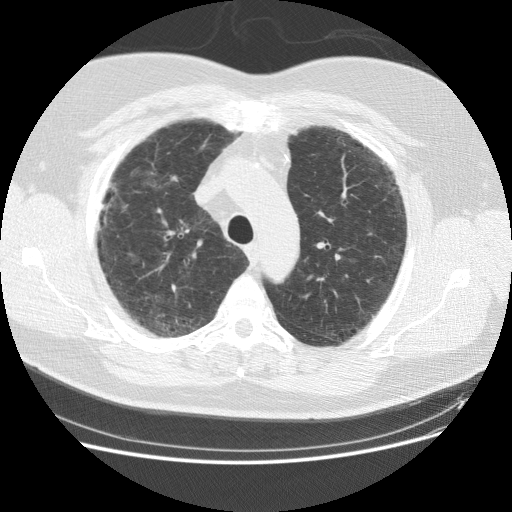
Chest CT (low-dose screening protocol), one axial image, baseline screening round, lung window (W 1500 / L -600 HU), 2.5 mm slice thickness, standard (soft-tissue) reconstruction kernel (STANDARD), 120 kVp, slice 33 of 151 in the series, 512 × 512 image matrix. Male, age 59 years at enrolment. Current smoker at enrolment.
Expert-annotated lung lesion, bounding box [x1, y1, x2, y2] px = [87, 165, 141, 231]. The screening reader recorded 2 non-calcified nodules or masses ≥4 mm on this exam (right middle lobe, right lower lobe); which of them this box marks is not recorded. Official screen result: positive, change unspecified: nodule(s) >= 4 mm or enlarging nodule(s), mass(es), or other non-specific abnormalities suspicious for lung cancer. Participant outcome: lung cancer diagnosed 338 days after this screen — adenocarcinoma, NOS, right upper lobe, right middle lobe, moderately differentiated (G2), stage IA (AJCC 6th edition), 13 mm at pathology.